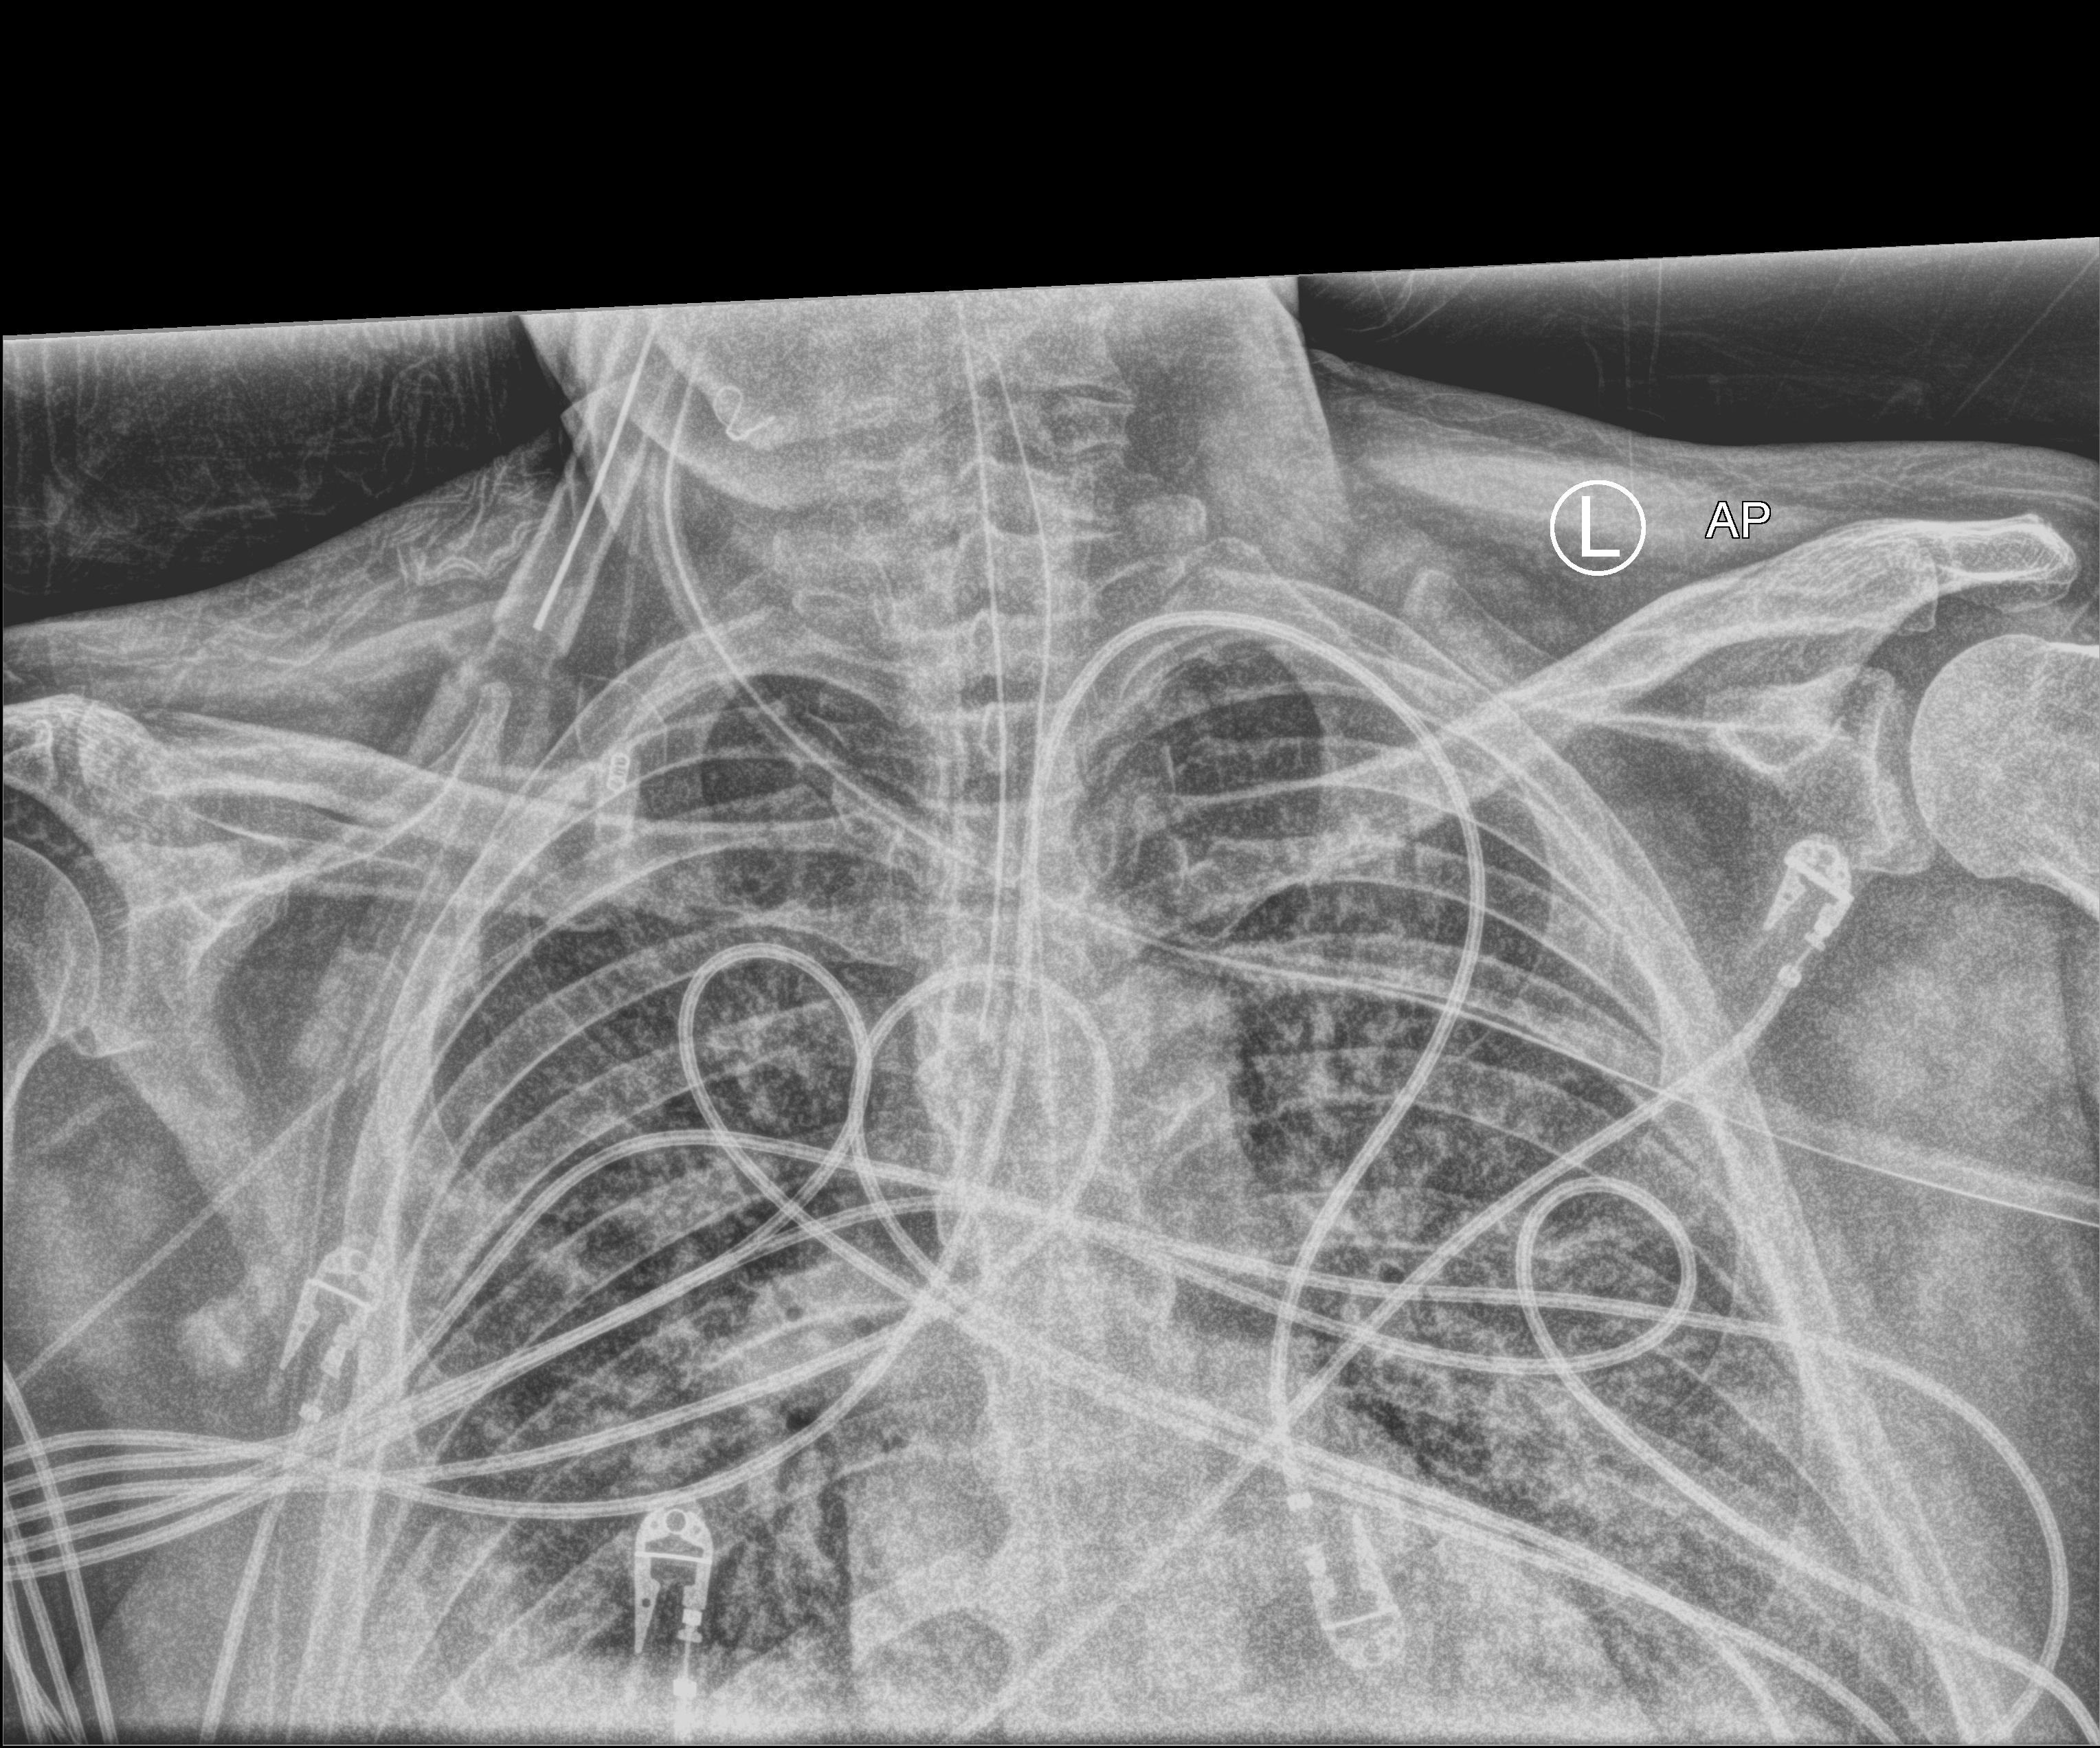
Portable chest radiograph, anteroposterior (AP) projection. Patient hospitalised with COVID-19; male, aged 60–74 years.
From the hospital-stay record, not from the radiograph (when in the stay this image was taken is not recorded):
- mechanically ventilated during this hospital stay: yes